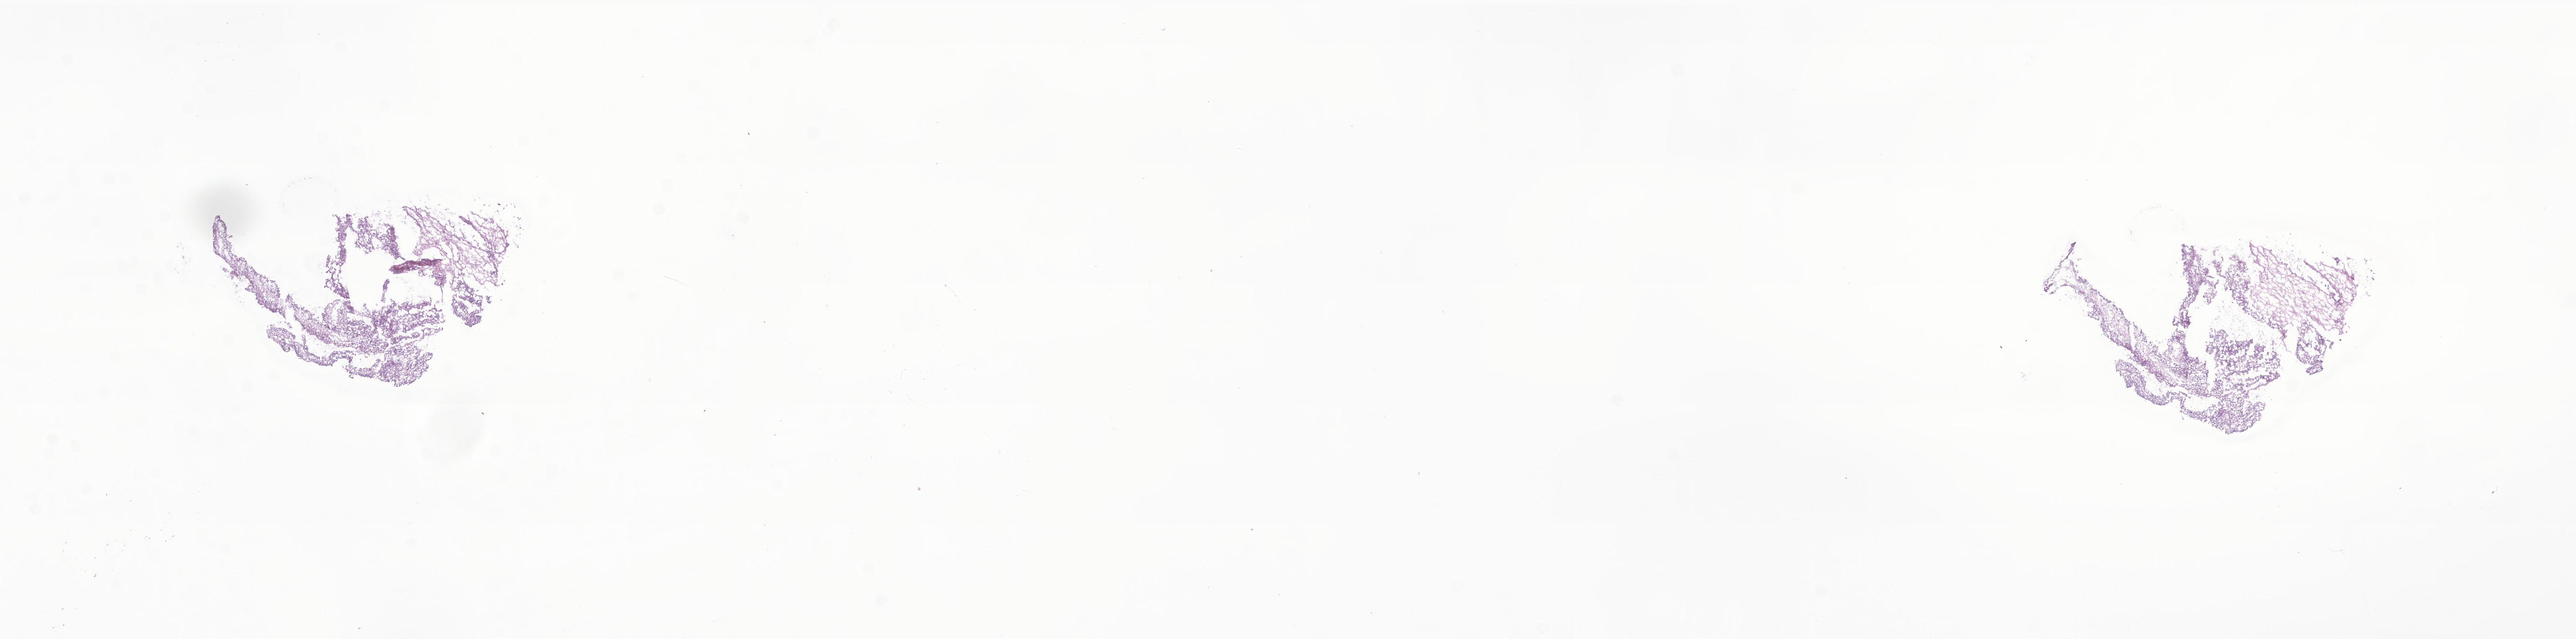
Digitized hematoxylin and eosin (H&E)-stained section of tumor tissue from the lower lobe of lung, shown as a low-resolution overview of the whole scanned area (about 22.9 x 5.7 mm). Frozen section (OCT-embedded). Patient: male, age 30 days.
• tissue or organ of origin (case record): lower lobe, lung
• recorded diagnosis: Pleuropulmonary blastoma